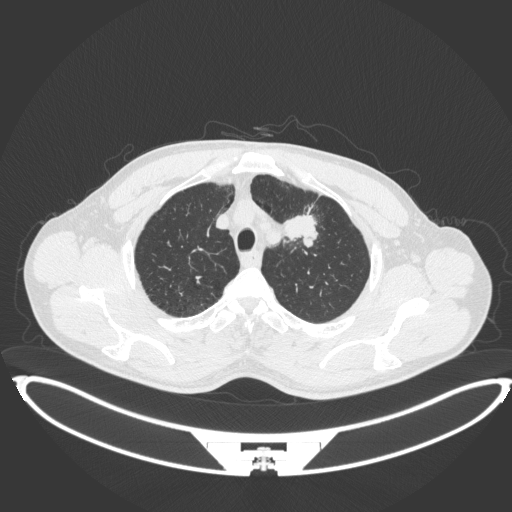
Chest CT, one axial slice. Slice 363 of 407 in the series (ordered by position). Lung window (W 1500 / L -600 HU). 1 mm slice thickness. 512 × 512 image matrix, field of view 457 × 457 mm. Male patient, age 60 years. From the clinical record (not read from this slice): clinical TNM (as recorded): T2a N0 M0; histopathological grade: G1-G2.
Outlined on this slice (bounding box drawn by a radiologist):
- lung tumour (recorded histology: squamous cell carcinoma): bounding box (x1, y1, x2, y2) in pixels: (278, 210, 321, 246)